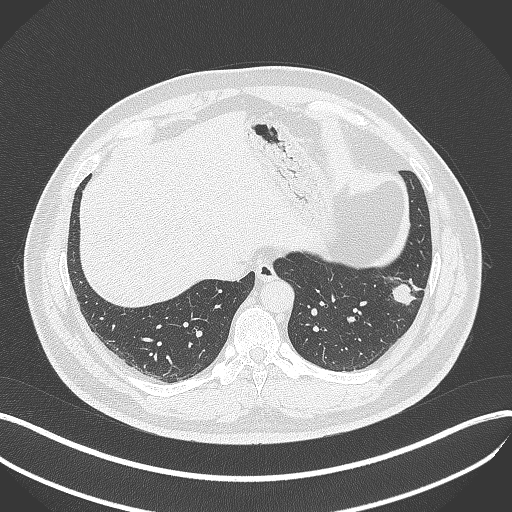
Chest CT, one axial slice. Slice 112 of 429 in the series (ordered by position). Reconstruction kernel B70f. Lung window (W 1500 / L -600 HU). 1 mm slice thickness. 512 × 512 image matrix. Patient: male, 39 years. From the clinical record (not read from this slice): clinical TNM (as recorded): T2a N0 M0.
Annotated regions visible in this slice (bounding box drawn by a radiologist):
- lung tumour (recorded histology: adenocarcinoma): bounding box [x1, y1, x2, y2] px = [387, 274, 421, 310]